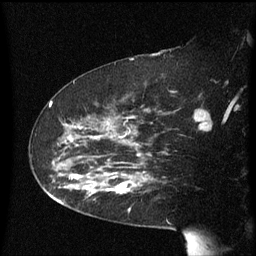
Breast MRI (dynamic contrast-enhanced), one sagittal slice. Position 39 of 60 along the scan axis. Dynamic contrast-enhanced series, image 2 of 3 at this slice position (ordered by acquisition). 1.5 T. TE 4.2 ms, TR 8.4 ms. 2.3 mm slice thickness. 256 × 256 image matrix. Female patient, age 63 years. Case-level facts recorded for this patient, not image findings: setting: breast cancer imaged before/during neoadjuvant chemotherapy; receptor status: HER2-positive.
Annotated regions visible in this slice (semi-automatic segmentation, software-assisted and operator-edited):
- analysis volume of interest (the breast-tissue region the enhancement analysis was run in; not a lesion): bounding box [x1, y1, x2, y2] px = [71, 144, 147, 199]
- tumour enhancement mask (voxels above the 70 % enhancement threshold inside the analysis volume of interest): [91, 154, 141, 195]